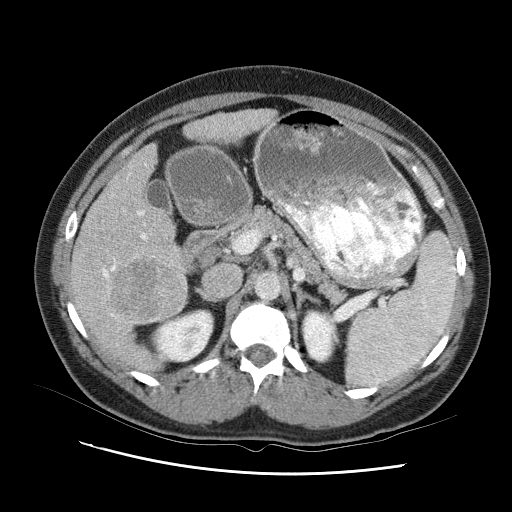
Contrast-enhanced abdominal CT (liver protocol), one axial slice; slice 50 of 95 in the series (ordered by position); one of 2 acquisitions stored at this slice position; soft-tissue window (W 400 / L 40 HU); 2.5 mm slice thickness; 512 × 512 image matrix, field of view 360 × 360 mm. Case-level facts recorded for this patient, not image findings: diagnosis: hepatocellular carcinoma (patient treated with transarterial chemoembolisation; whether this scan precedes or follows treatment is not stated here); TNM stage (as recorded): Stage-I; Child-Pugh class: B; tumour differentiation: moderately differentiated; tumour nodularity: uninodular.
Structures marked on this image (semi-automatic segmentation, software-assisted and operator-edited):
- liver parenchyma outside the tumour (the mass and vessels are separate outlines, so this box may not span the whole liver): bounding box [x1, y1, x2, y2] px = [66, 102, 284, 372]
- mass: [121, 254, 190, 319]
- liver vessels: [91, 181, 165, 372]